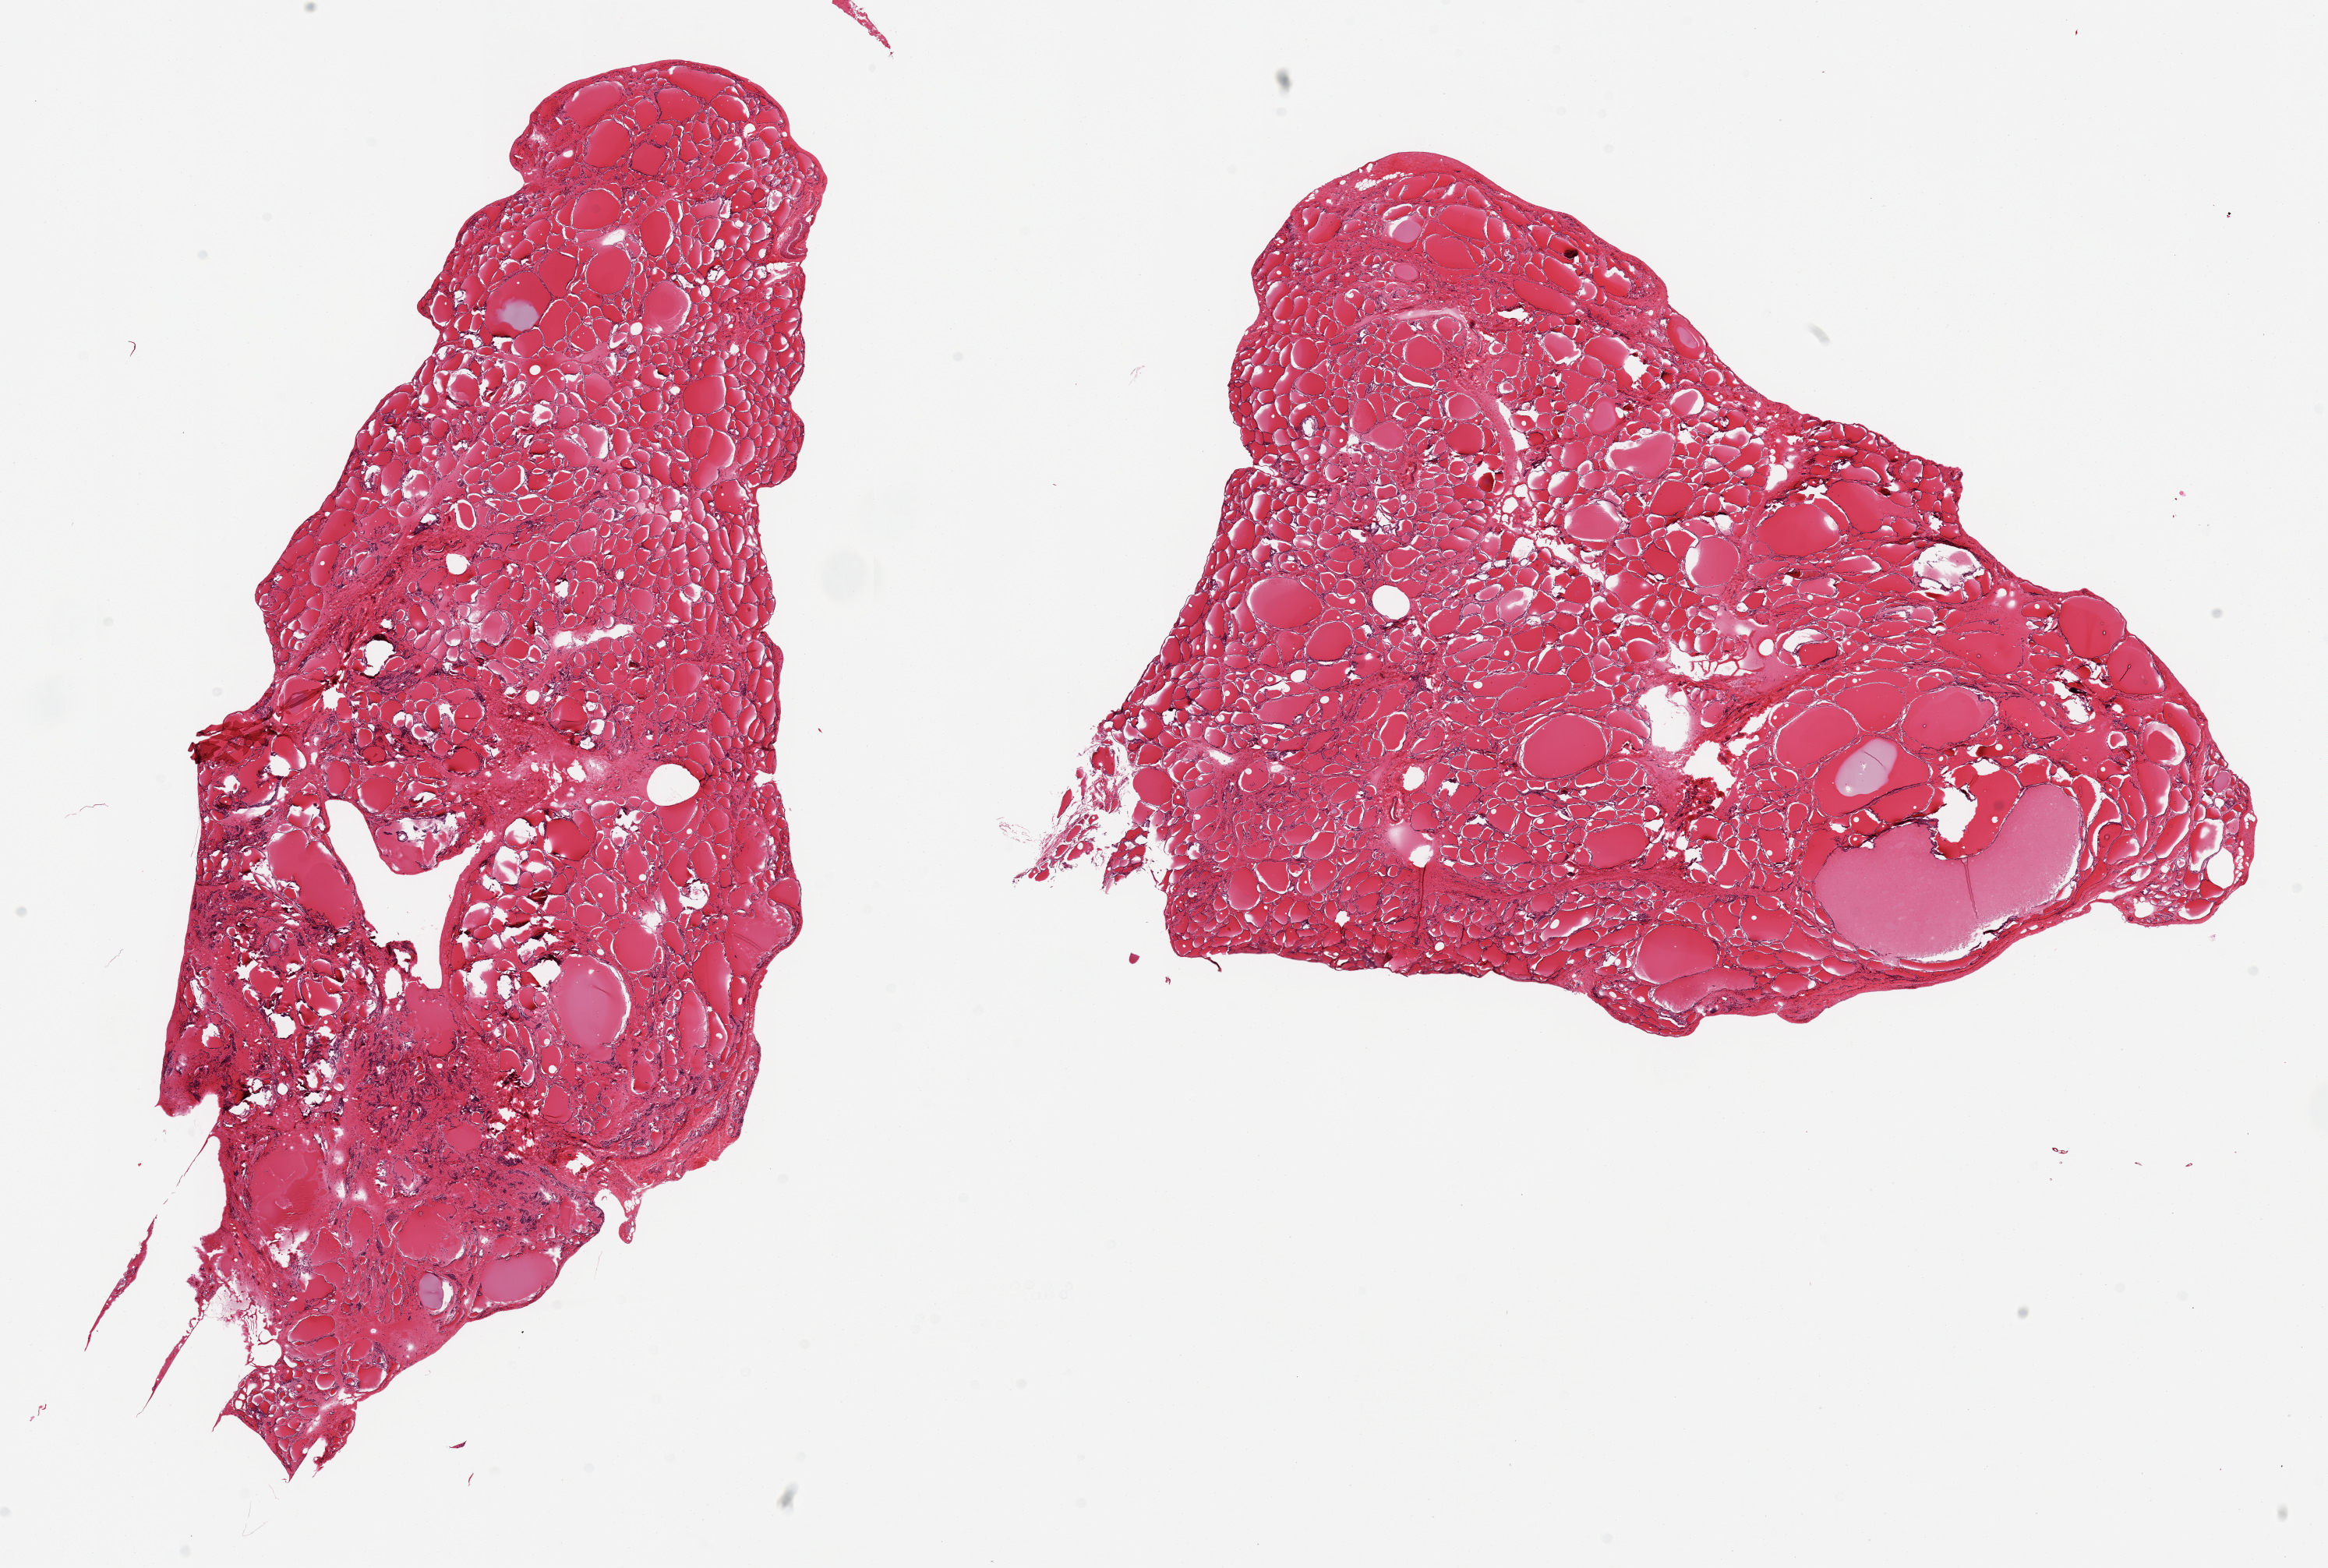
H&E whole-slide image, shown as a low-resolution overview of the whole scanned area (about 23.6 x 15.9 mm), PAXgene-fixed paraffin-embedded (PFPE) section, section of thyroid (target tissue), donor tissue sample. Donor sex: male.
* reviewer comment on this tissue sample: 2 pieces